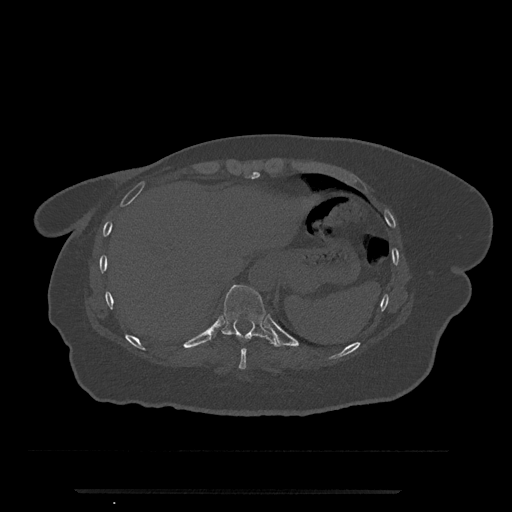
CT including the spine, one axial slice; position 303 of 797 along the scan axis; reconstruction kernel Br40s/3; bone window (W 1800 / L 400 HU); 0.5 mm slice thickness; 512 × 512 image matrix, field of view 440 × 440 mm. Patient: female, 51 years. From the clinical record (not read from this slice): primary cancer: neuro; vertebrae with lytic lesions (as recorded): T8.
Structures marked on this image (semi-automatically segmented with operator editing):
- T10 vertebra: bounding box <221,285,278,347> (left, top, right, bottom; pixels)
- T9 vertebra: <239,348,247,370>